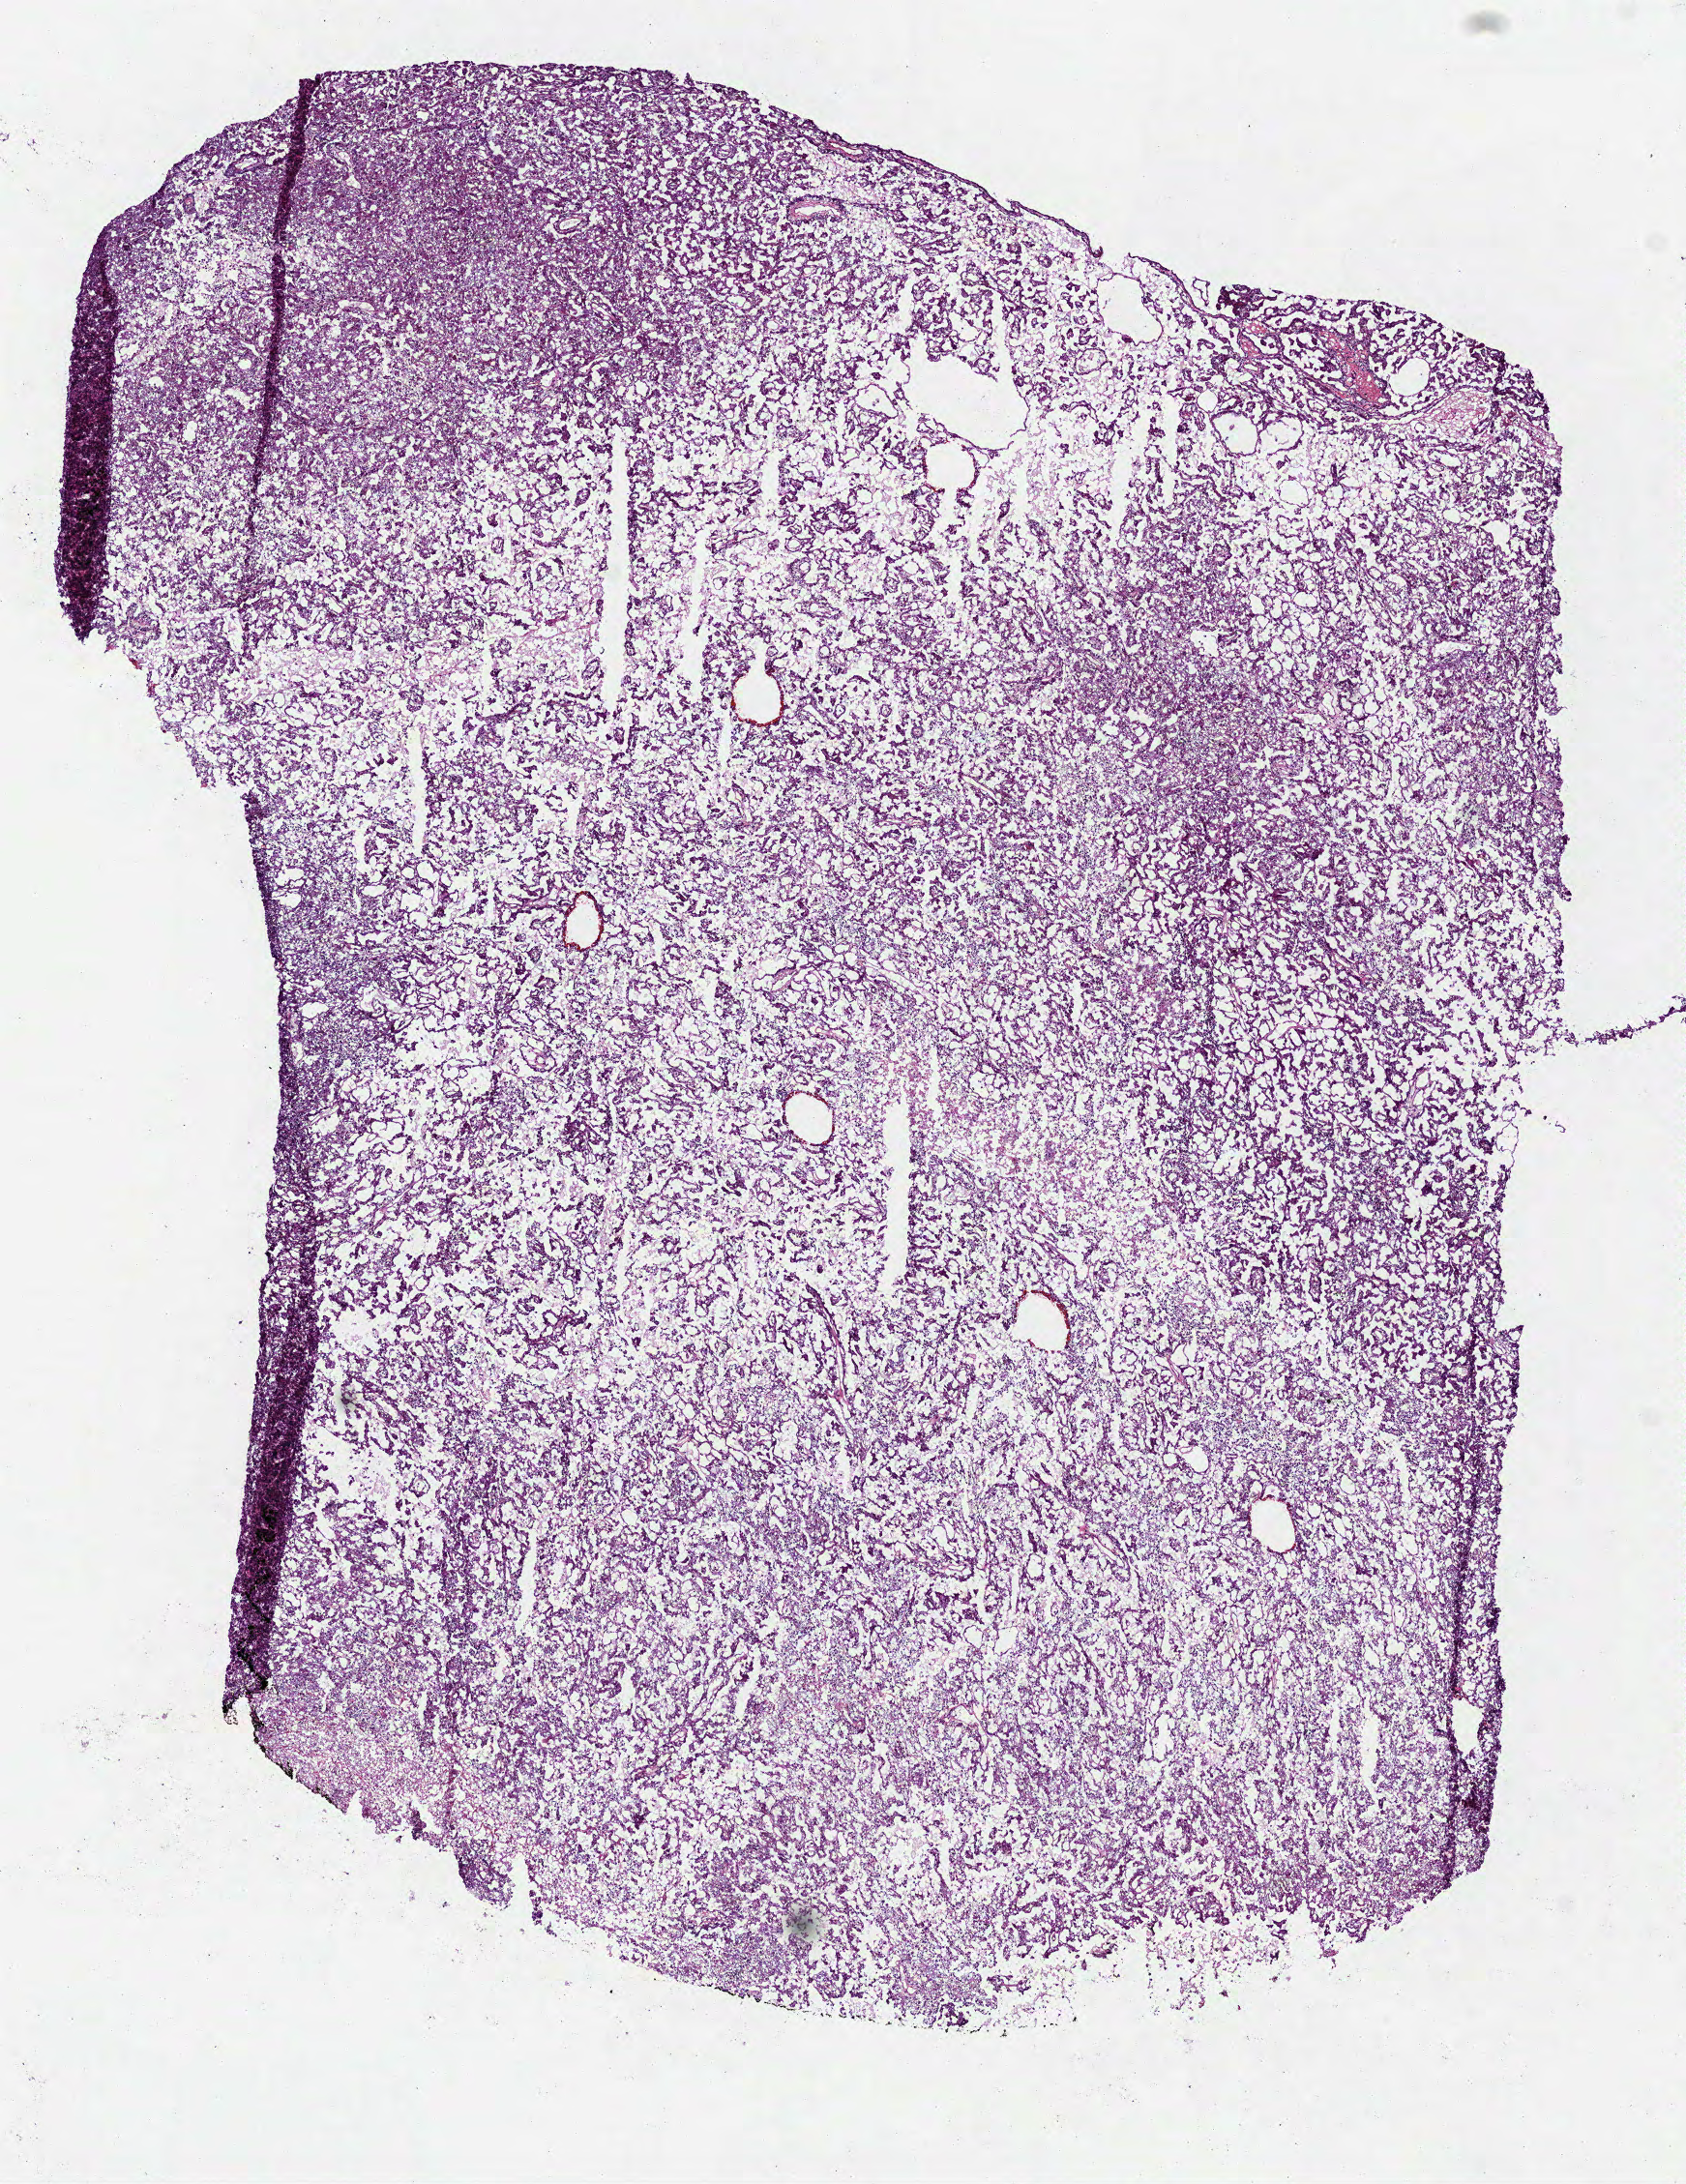
Whole-slide histology image, Hematoxylin and eosin (H&E) stained, shown as a low-resolution overview of the whole scanned area (about 7.0 x 9.1 mm); frozen section; primary tumour sample from the kidney. Patient: male, age at initial diagnosis 67 years.
AJCC pathologic stage: I (7th edition). Laterality: left. Pathologic diagnosis: Papillary adenocarcinoma, NOS.